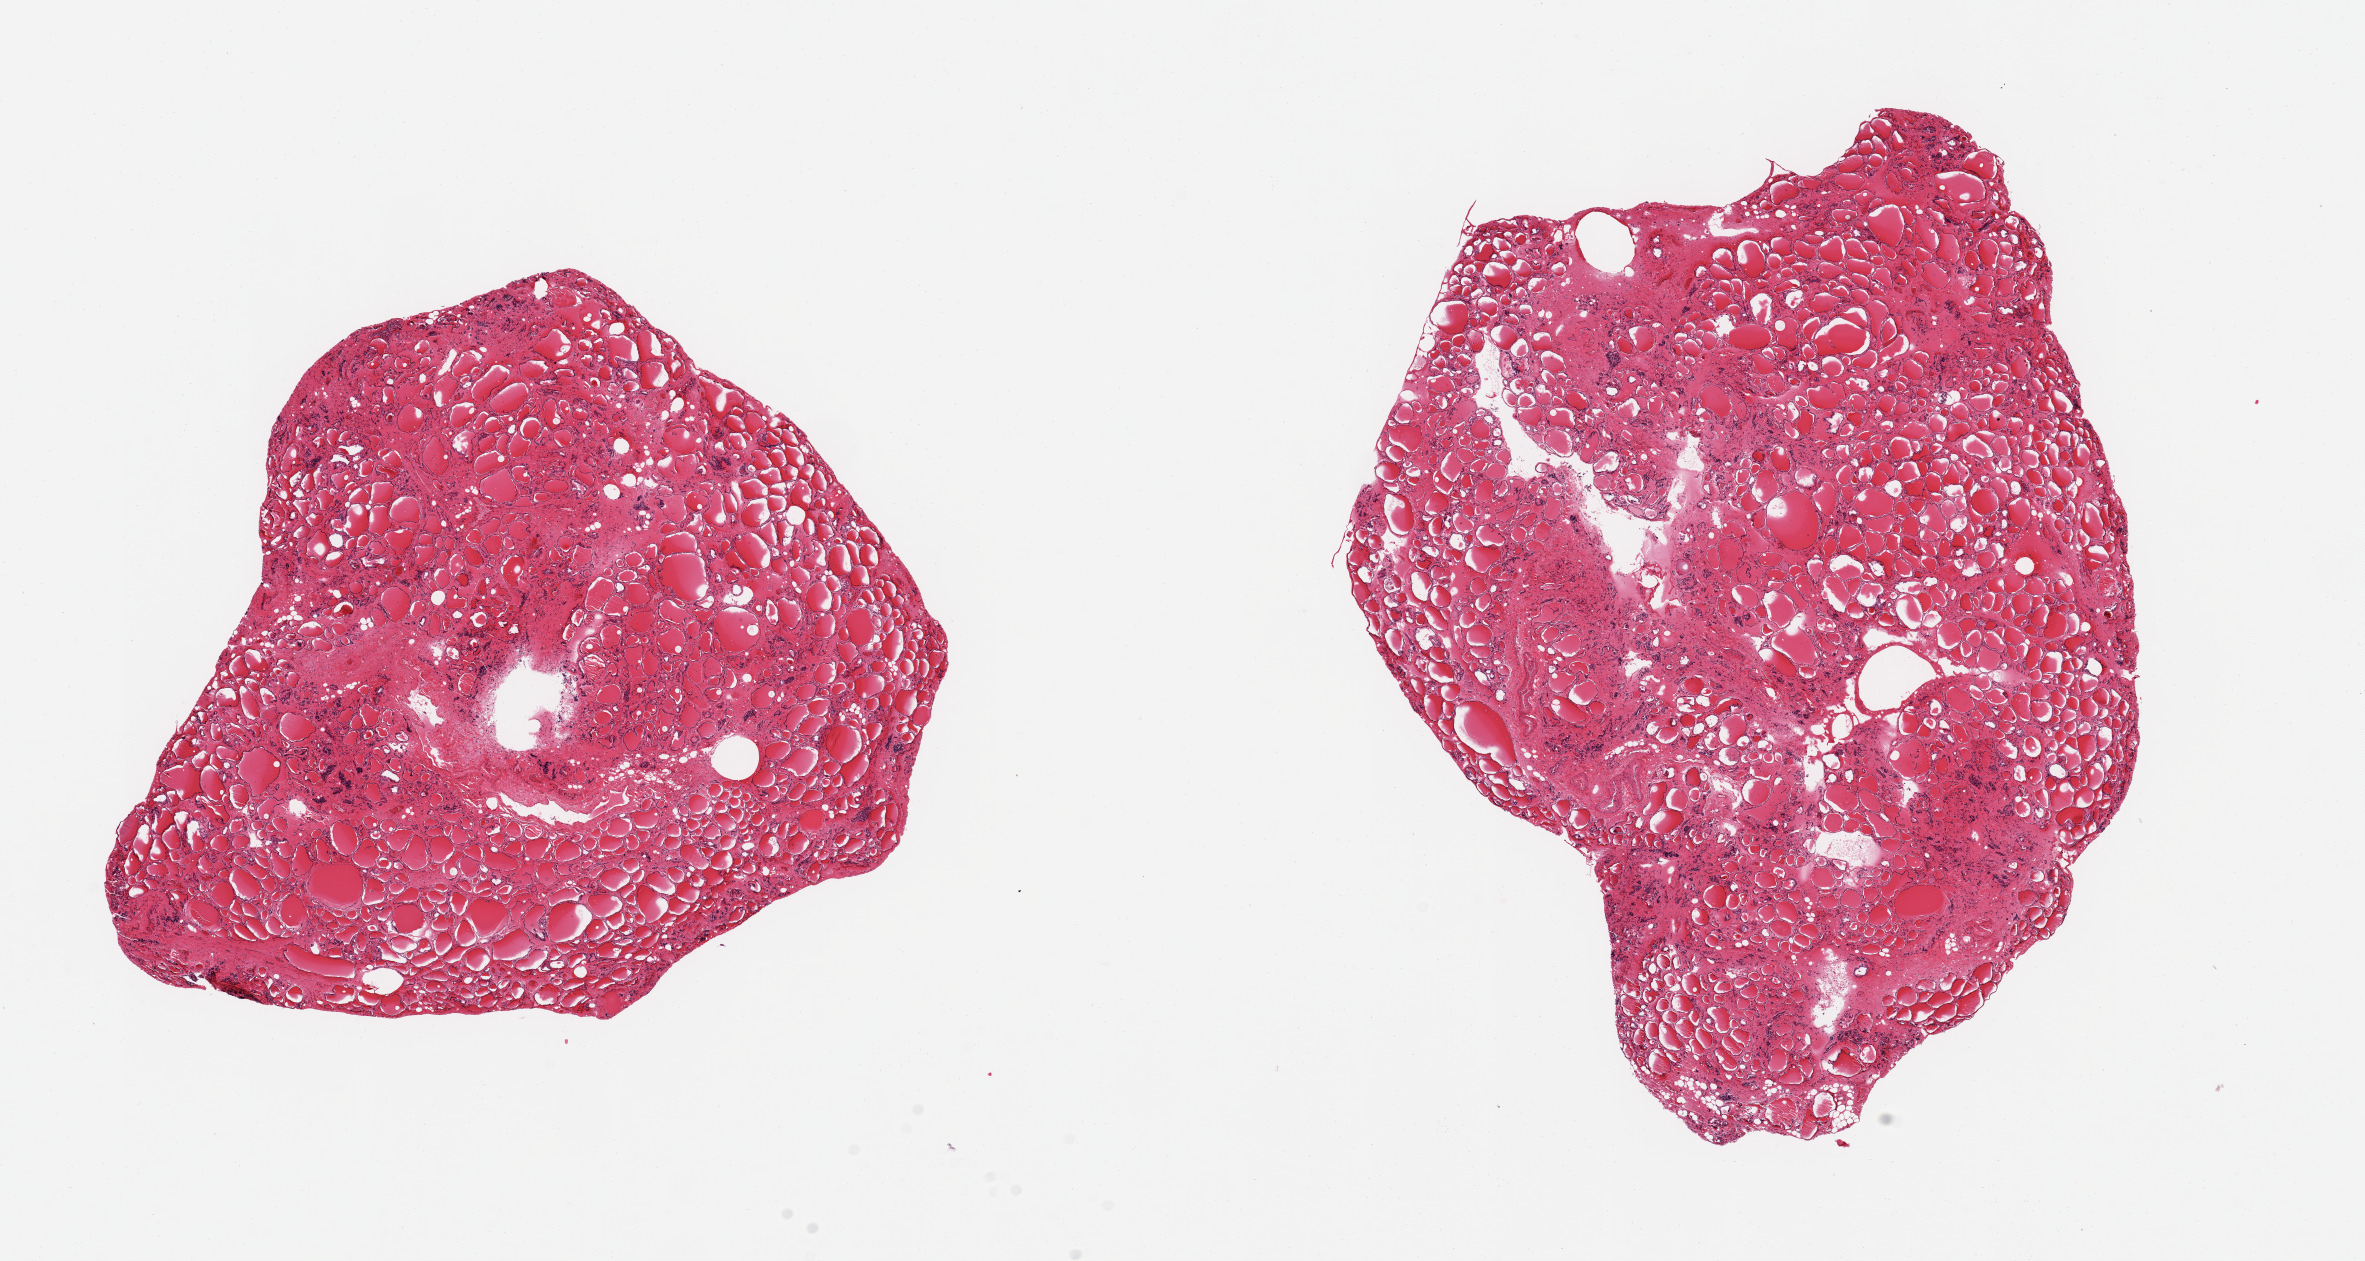
Whole-slide image, haematoxylin and eosin stain — a low-resolution overview of the entire scanned area, about 18.7 x 10.0 mm (acquisition: 20x scan); PAXgene-fixed, paraffin-embedded tissue; section of thyroid (target tissue); tissue donor sample. Donor: male.
Pathologist's review note for this sample: 2 pieces, no abnnormalities.